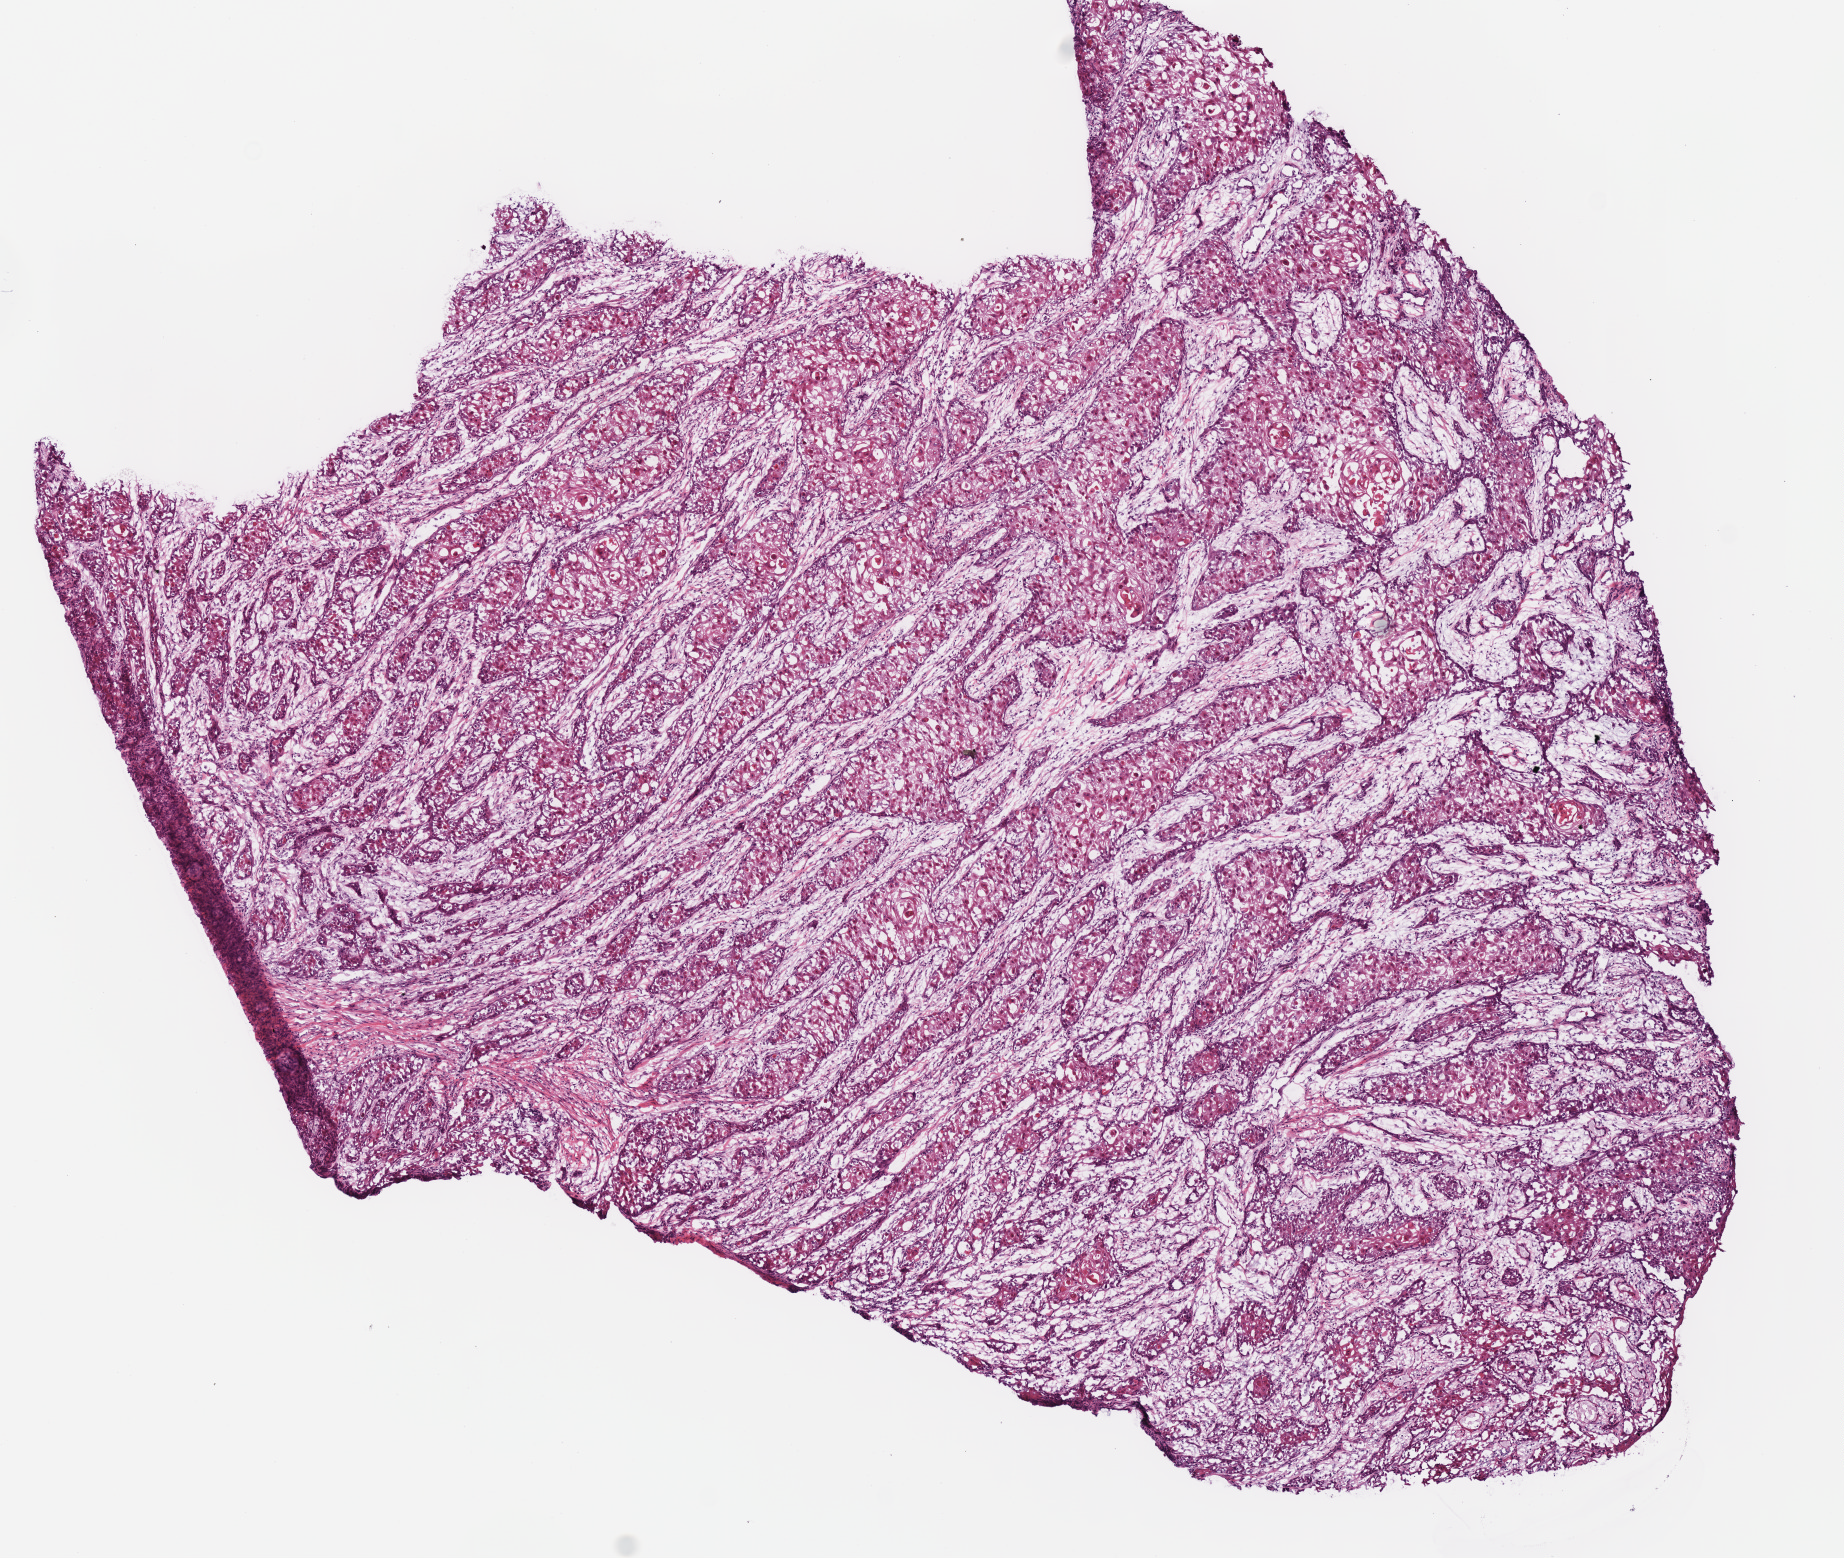
H&E-stained whole-slide image, a low-resolution overview of the entire scanned area, about 7.3 x 6.1 mm; frozen section; head and neck, primary tumour sample. Patient: male, age at initial diagnosis 64 years.
Diagnosis: Squamous cell carcinoma, NOS (overlapping lesion of lip, oral cavity and pharynx).